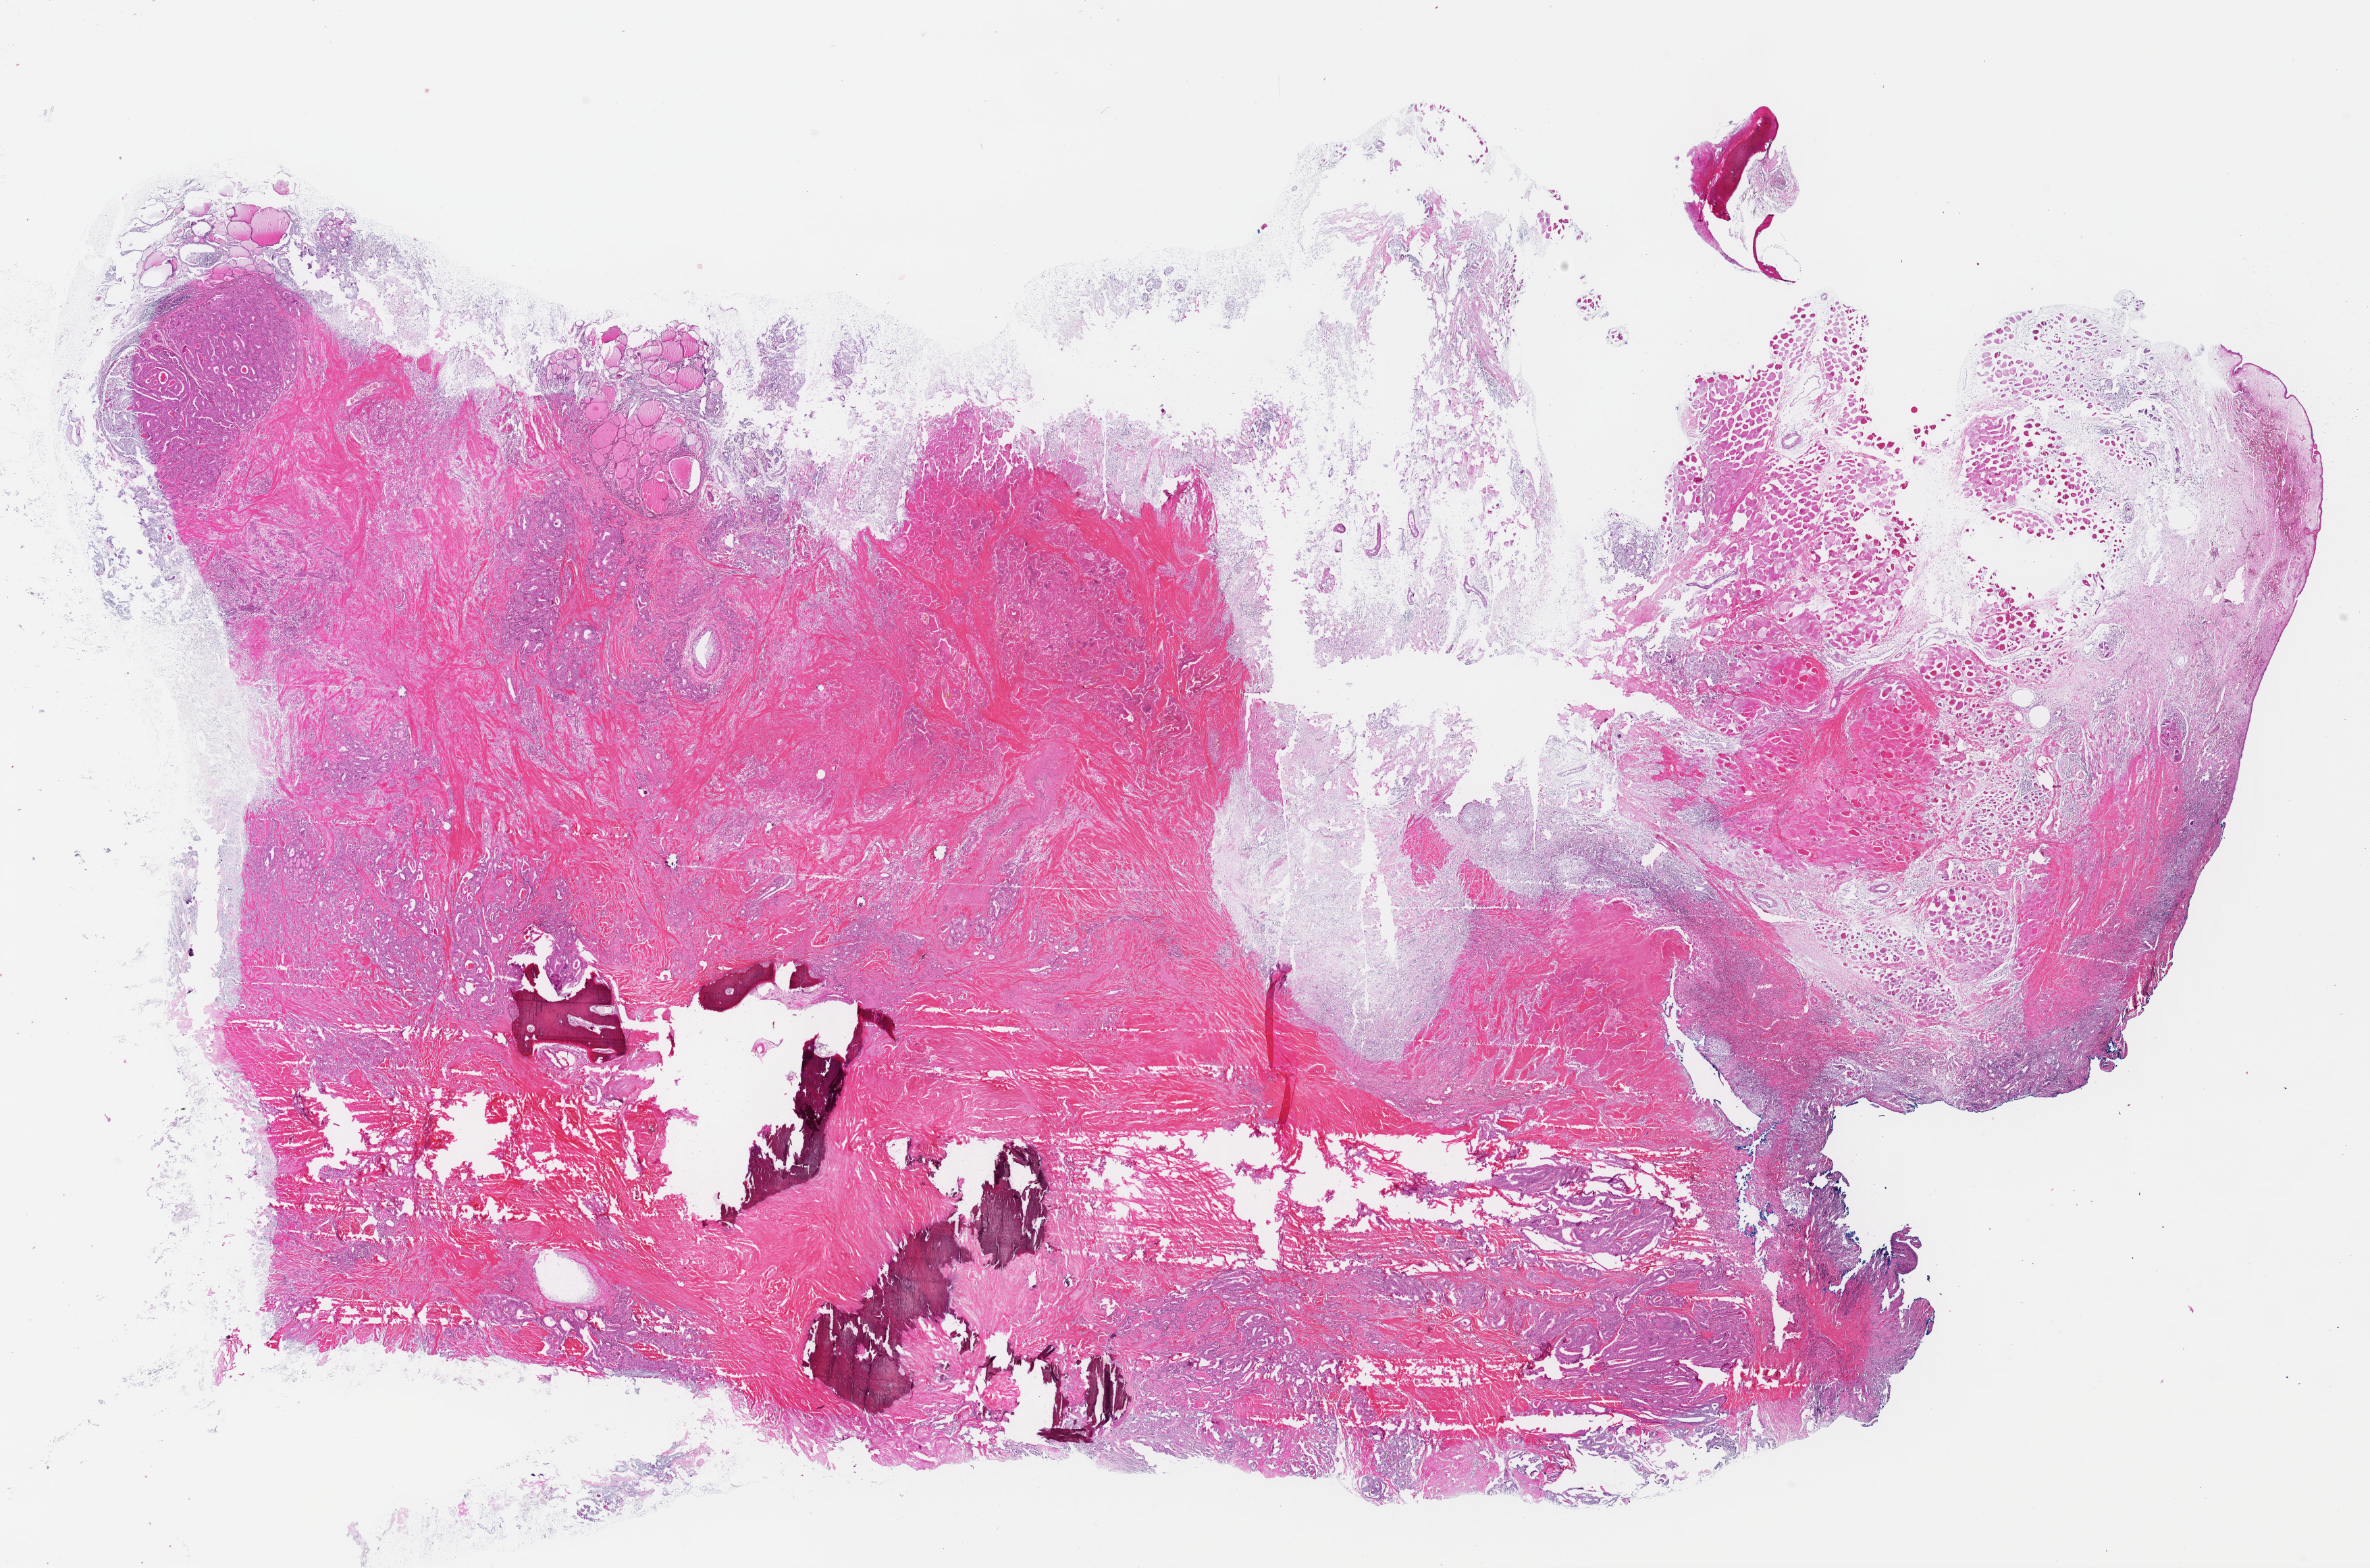
Digitized Hematoxylin and eosin (H&E) stained tissue section (whole slide), a low-resolution overview of the entire scanned area, about 27.6 x 18.3 mm, formalin-fixed paraffin-embedded (FFPE) diagnostic section, thyroid, primary tumour sample. Male patient; age at initial diagnosis 66 years.
Lymph nodes positive (case pathology): 1 of 2 examined. Histologic diagnosis: Papillary adenocarcinoma, NOS (thyroid gland). Laterality: left. AJCC pathologic stage: III (5th edition).